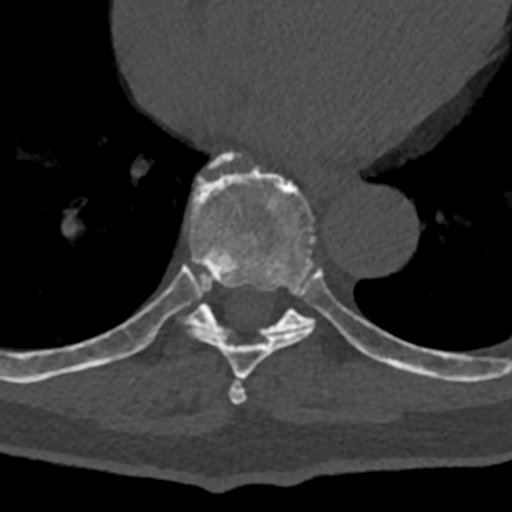
CT including the spine, one axial slice. Position 689 of 797 along the scan axis. Reconstruction kernel Br40s/3. 120 kVp. Bone window (W 1800 / L 400 HU). 0.5 mm slice thickness. 512 × 512 image matrix, field of view 160 × 160 mm. Patient: male, 74 years. From the clinical record (not read from this slice): primary cancer: renal; vertebrae with lytic lesions (as recorded): T10, L1, L2, L3, L4, L5.
Annotated regions visible in this slice (semi-automatic segmentation, software-assisted and operator-edited):
- T7 vertebra: box from (x=229, y=377) to (x=247, y=404) px
- T8 vertebra: (x=70, y=153)–(x=385, y=379)
- T9 vertebra: (x=104, y=152)–(x=432, y=377)